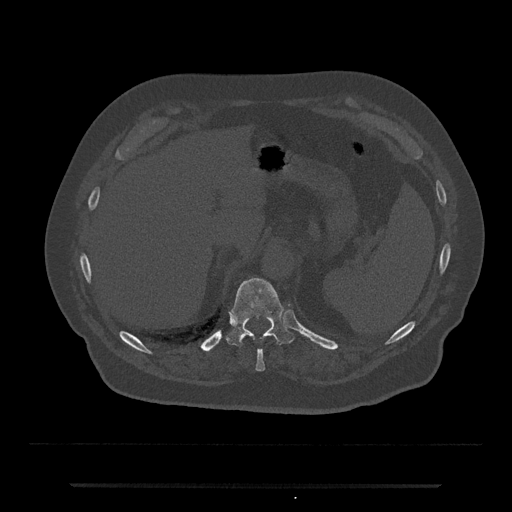
CT including the spine, one axial slice. Position 664 of 797 along the scan axis. 120 kVp. Bone window (W 1800 / L 400 HU). 0.5 mm slice thickness. 512 × 512 image matrix, field of view 434 × 434 mm. Patient: male, 80 years. Case-level facts recorded for this patient, not image findings: primary cancer: prostate.
Outlined on this slice (semi-automatically segmented with operator editing):
- T10 vertebra: bounding box [x1, y1, x2, y2] px = [255, 350, 265, 371]
- T11 vertebra: [226, 278, 295, 346]